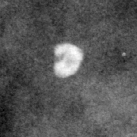
Cropped region of a digitized screen-film mammogram centred on a radiologist-marked abnormality; right breast; CC view.
Finding: calcifications, morphology coarse / round and regular / lucent centered; BI-RADS assessment category 2; benign; no additional work-up was recommended (benign without callback).